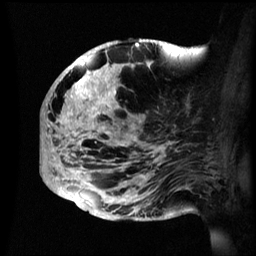
Breast MRI (dynamic contrast-enhanced), one sagittal slice. Slice 26 of 60 in the series (ordered by position). Dynamic contrast-enhanced series, image 2 of 3 at this slice position (ordered by acquisition). 1.5 T. TE 4.2 ms, TR 8.4 ms. 256 × 256 image matrix. Female patient, age 48 years.
Structures marked on this image (semi-automatic segmentation, software-assisted and operator-edited):
- analysis volume of interest (the breast-tissue region the enhancement analysis was run in; not a lesion): bounding box [x1, y1, x2, y2] px = [42, 41, 195, 221]
- tumour enhancement mask (voxels above the 70 % enhancement threshold inside the analysis volume of interest): [42, 41, 177, 219]